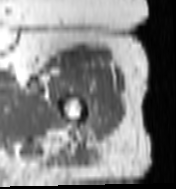
MRI of an extremity soft-tissue mass, one axial slice; slice 93 of 100 in the series (ordered by position); MR volume resampled by the dataset authors to the PET/CT grid (not the native acquisition matrix); 3.27 mm slice thickness; 176 × 189 image matrix. Female patient. From the clinical record (not read from this slice): histological type: undifferentiated – high grade; grade: high; site of the primary tumour: left thigh.
Structures marked on this image (expert contour drawn on MRI and transferred to this co-registered scan by the dataset authors):
- gross tumour volume including surrounding oedema: box from (x=89, y=105) to (x=108, y=124) px